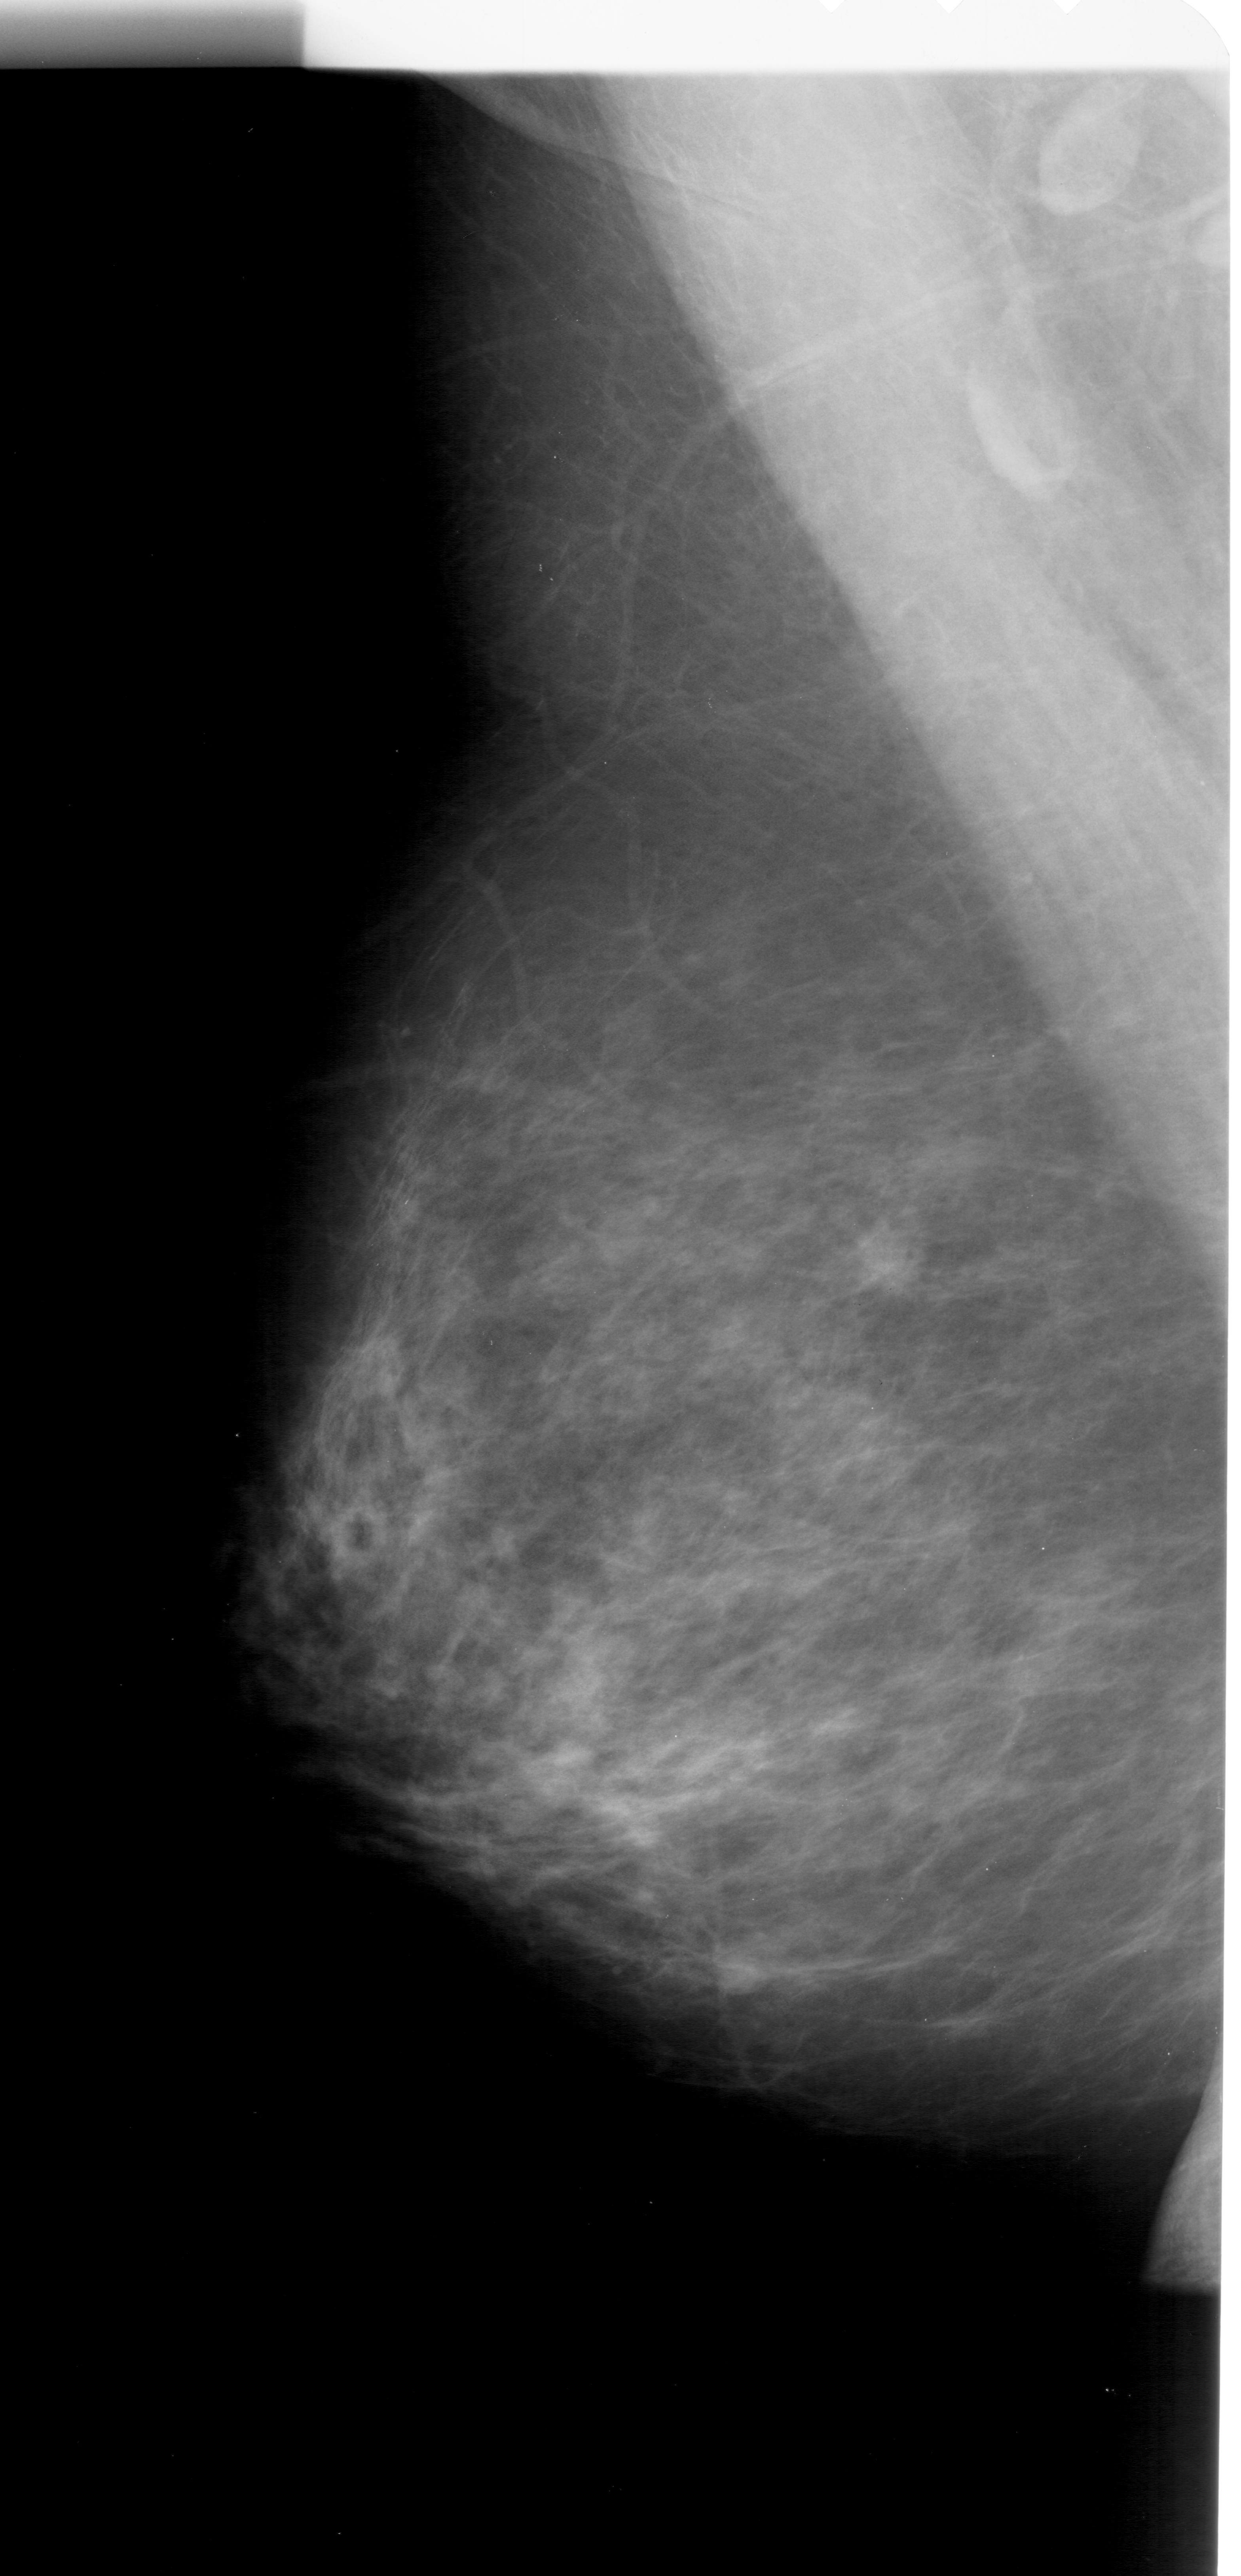
Mammogram (digitized film), left breast, mediolateral oblique (MLO) view, BI-RADS breast density category 3 (scale 1–4).
Marked findings (only marked abnormalities are described; nothing is implied about the rest of the image): mass, shape irregular, margins ill defined; BI-RADS assessment category 4; subtlety rating 1 on a 1 (subtle) to 5 (obvious) scale; pathology result (as recorded, not read from the image): malignant.